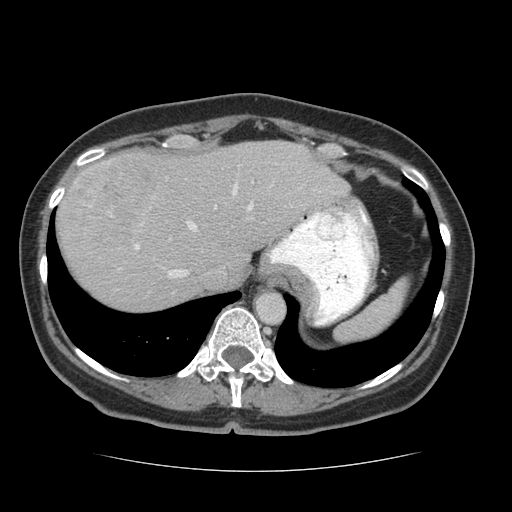
Contrast-enhanced abdominal CT (liver protocol), one axial slice; slice 54 of 75 in the series (ordered by position); reconstruction kernel STANDARD; 140 kVp; soft-tissue window (W 400 / L 40 HU); 512 × 512 image matrix, field of view 360 × 360 mm. Case-level facts recorded for this patient, not image findings: diagnosis: hepatocellular carcinoma (patient treated with transarterial chemoembolisation; whether this scan precedes or follows treatment is not stated here); TNM stage (as recorded): Stage-I.
Annotated regions visible in this slice (semi-automatically segmented with operator editing):
- abdominal aorta: box from (x=256, y=293) to (x=285, y=324) px
- liver parenchyma outside the tumour (the mass and vessels are separate outlines, so this box may not span the whole liver): (x=56, y=140)–(x=348, y=310)
- mass: (x=70, y=154)–(x=172, y=249)
- liver vessels: (x=134, y=183)–(x=272, y=278)